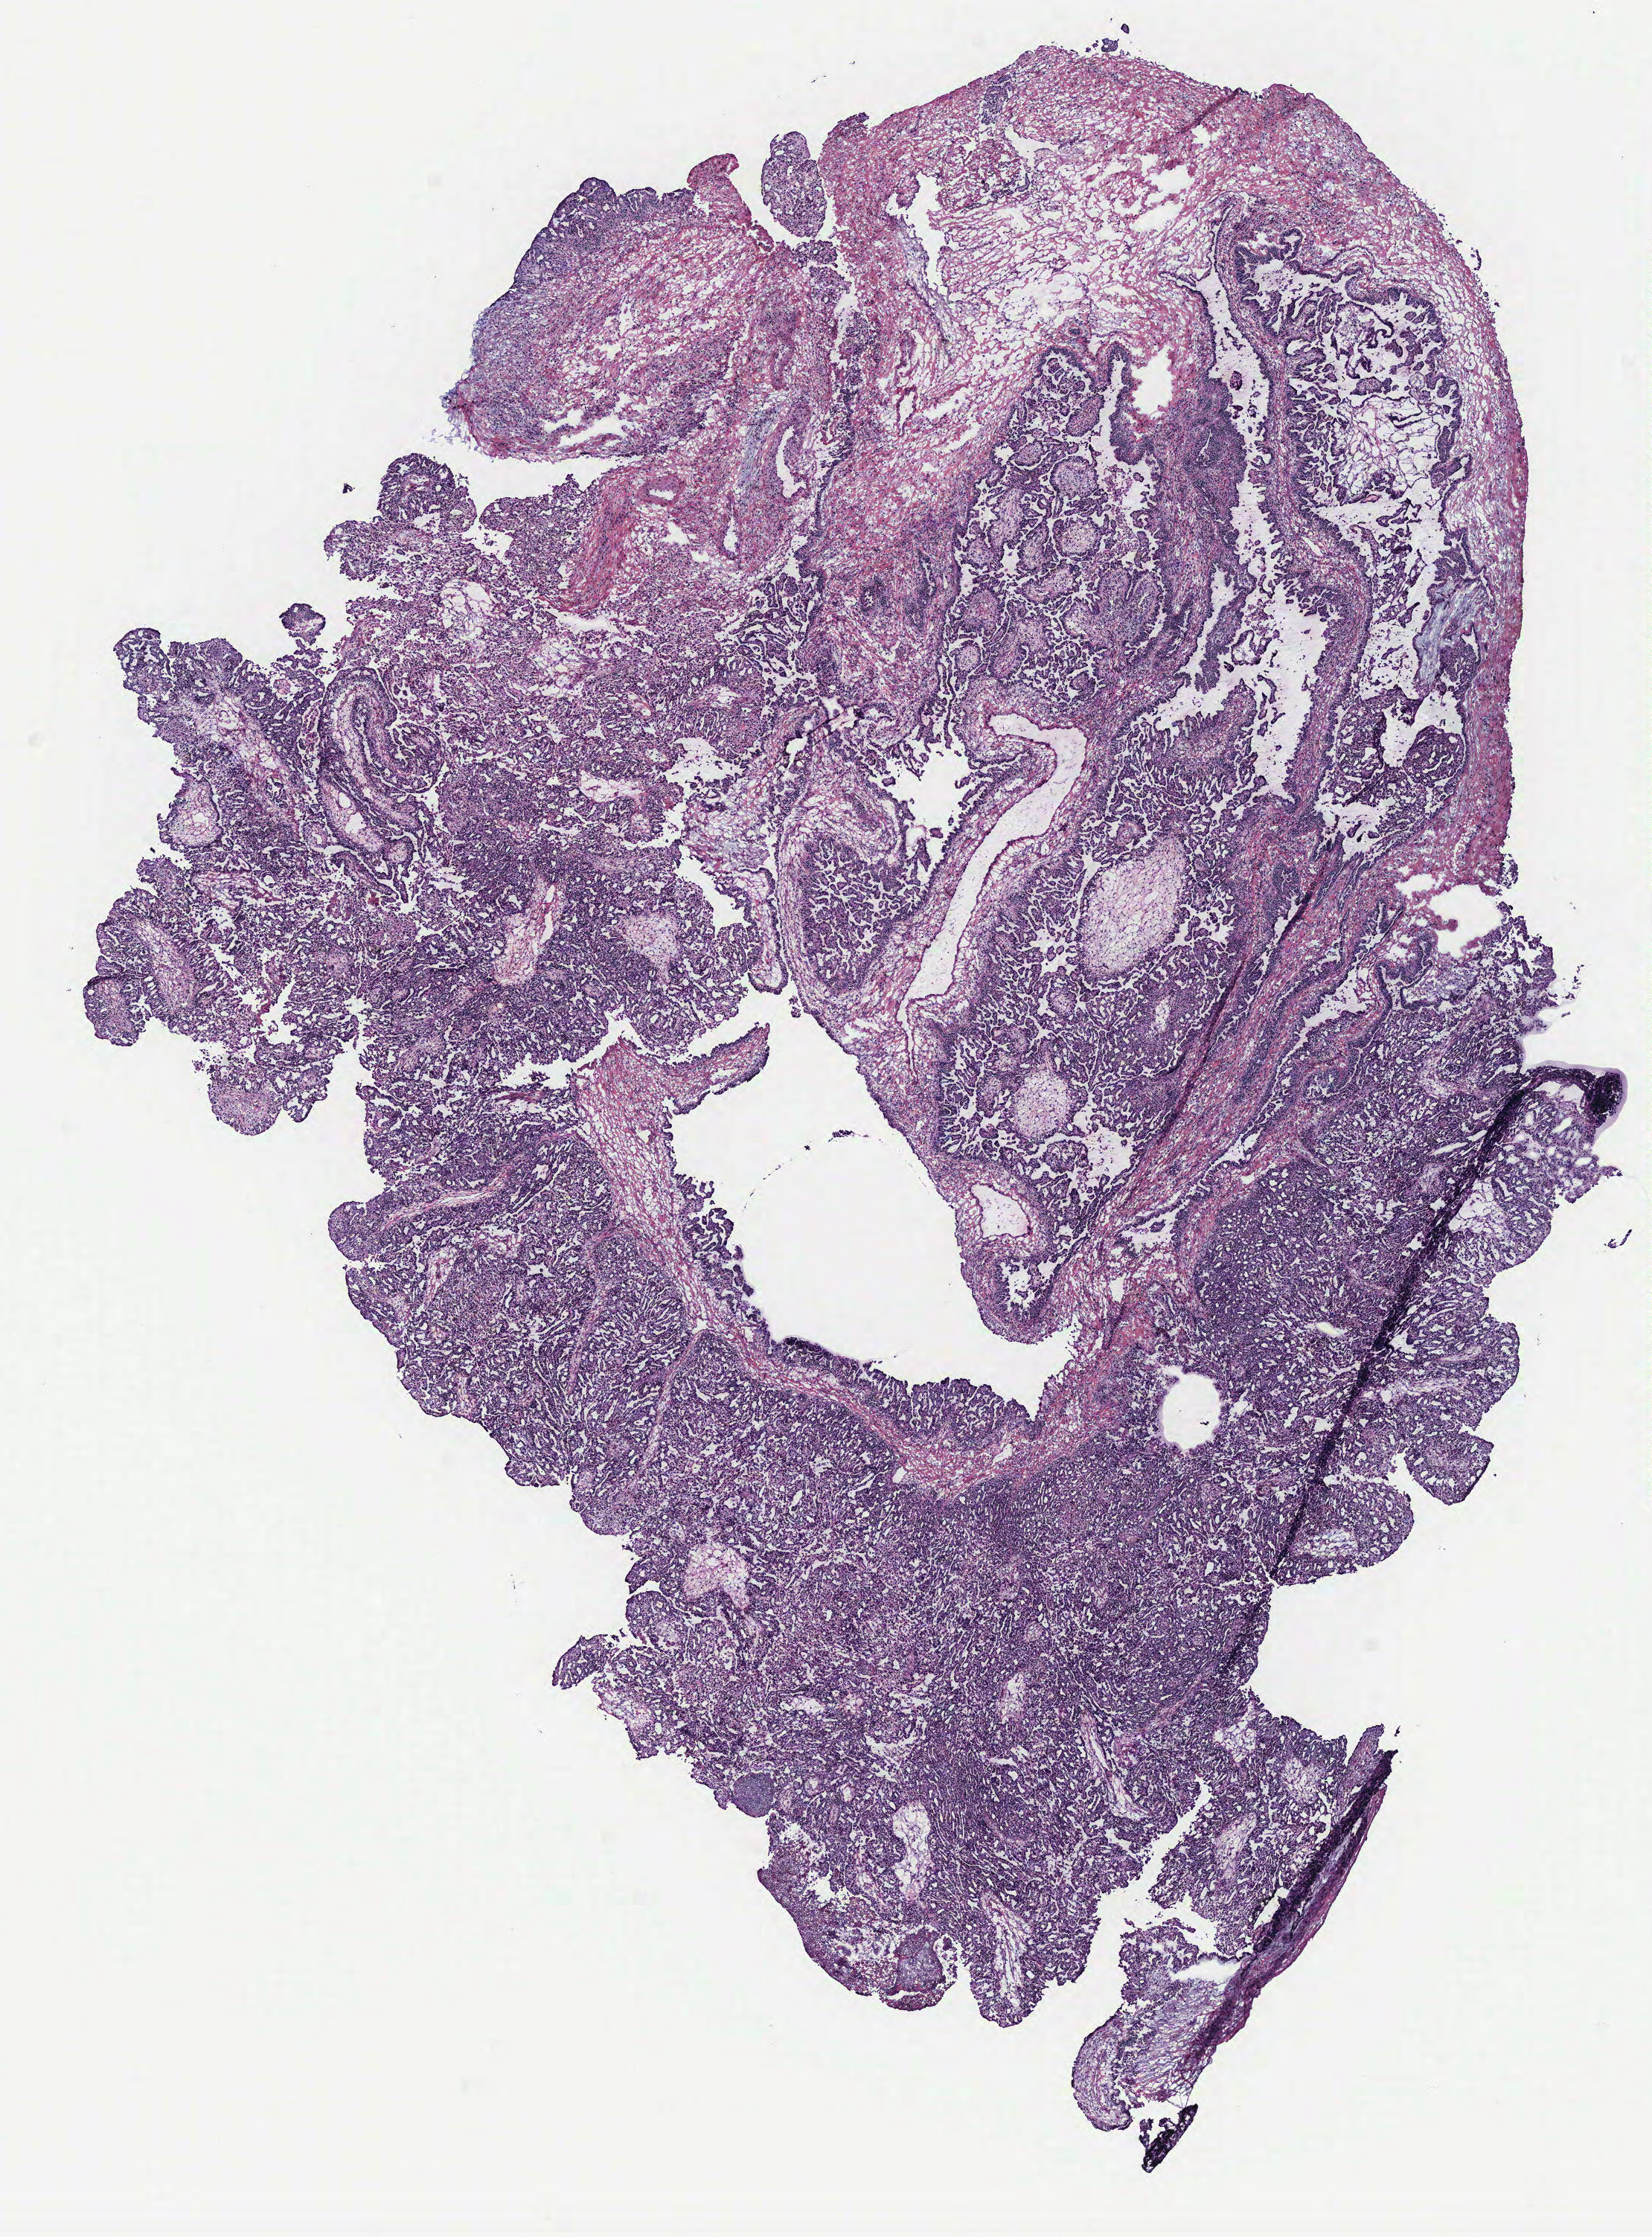
H&E-stained whole-slide image — shown as a low-resolution overview of the whole scanned area (about 8.9 x 12.0 mm, from a 40x scan), ovary, tissue type not recorded. Patient sex: female.
* patient diagnosis: Serous adenocarcinoma, NOS